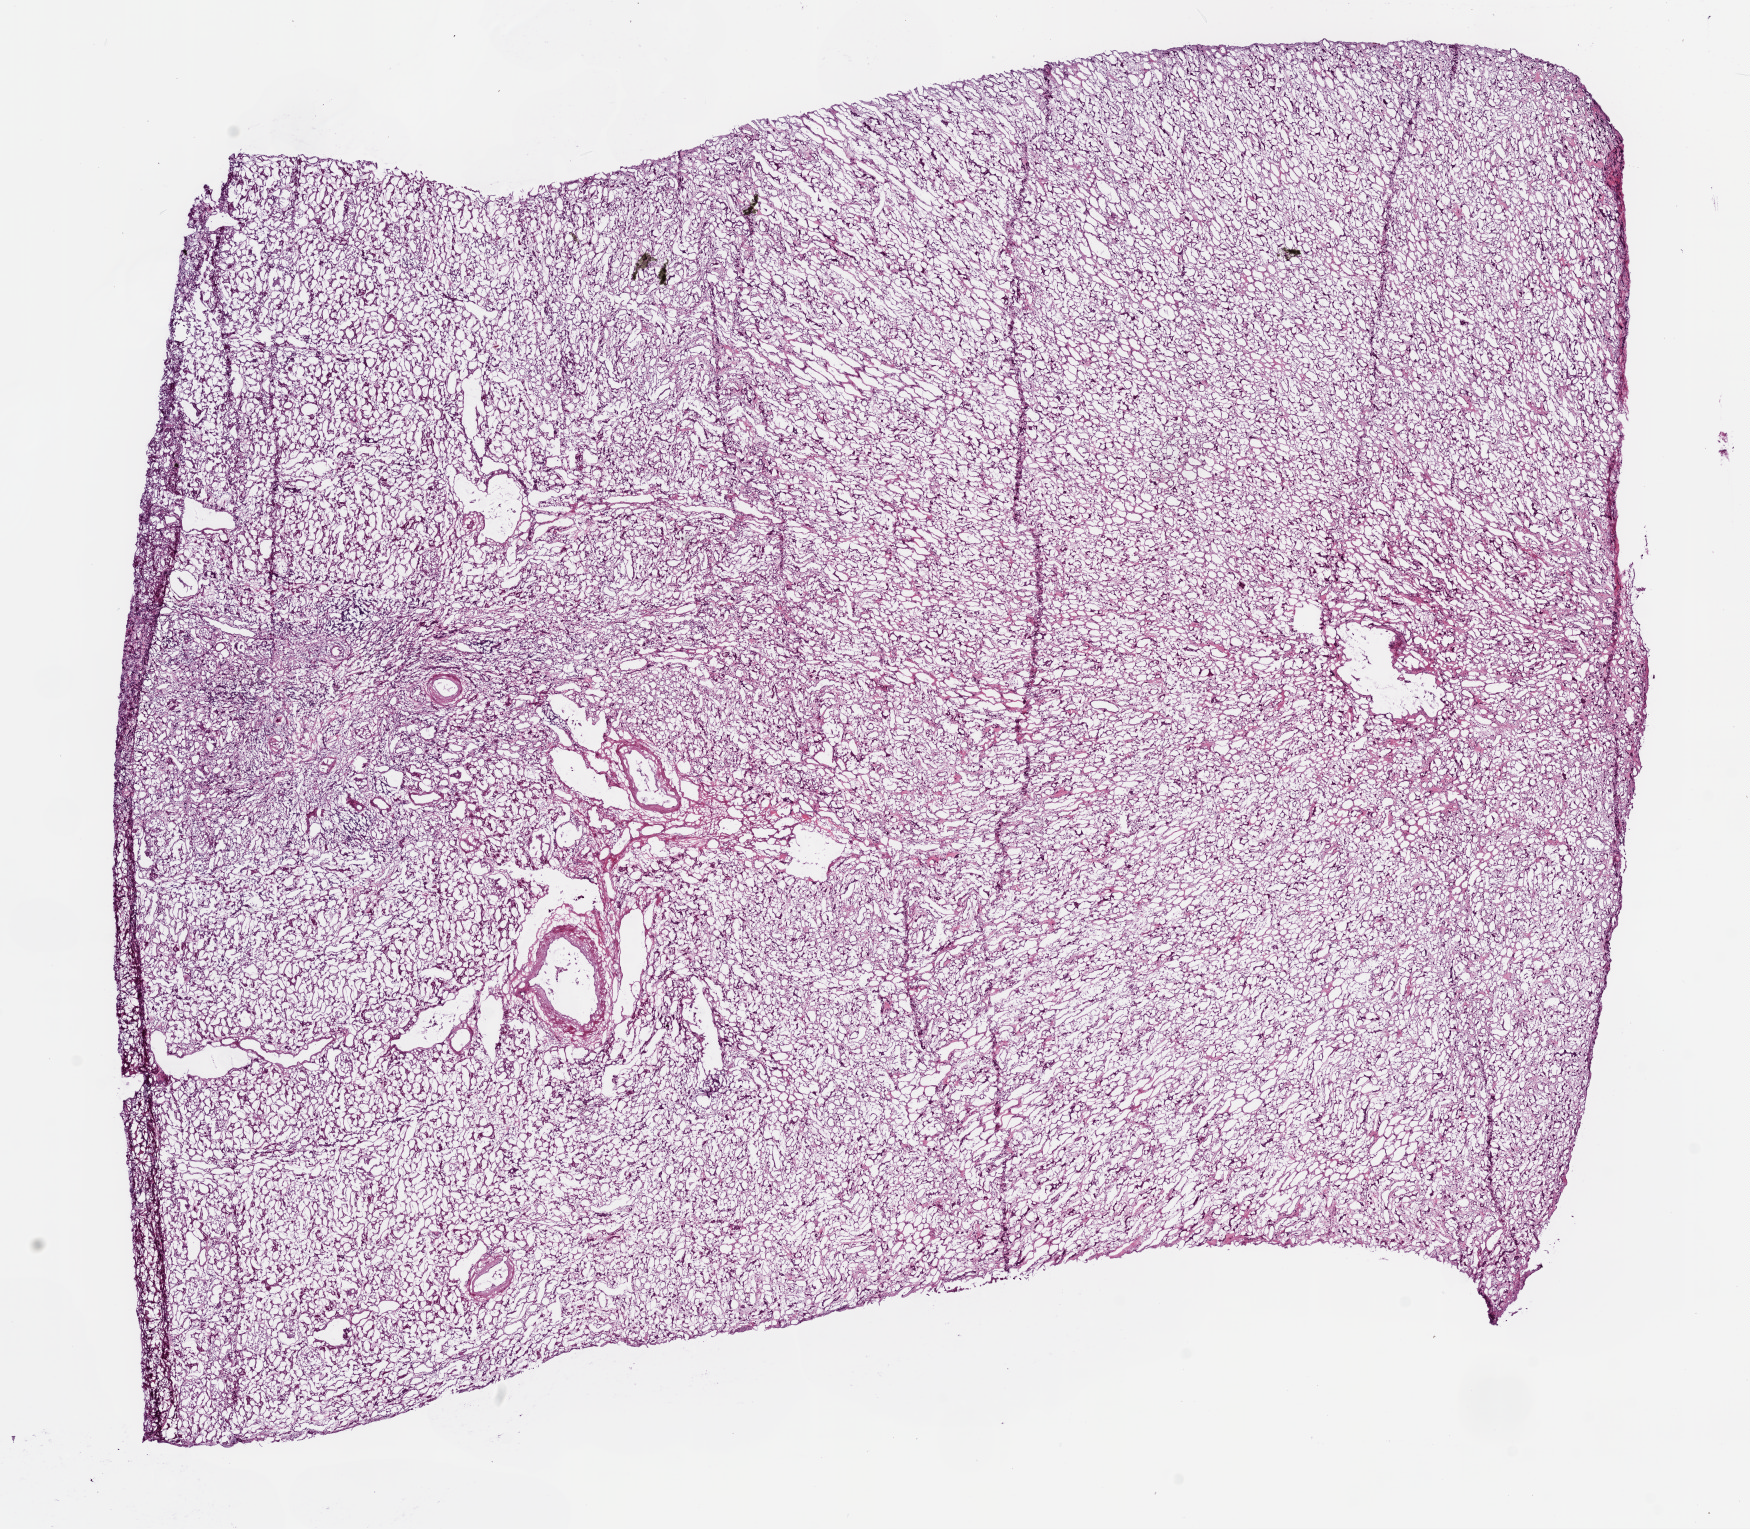
Whole-slide histology image, Hematoxylin and eosin (H&E) stained, low-resolution overview of the scanned area, about 14.0 x 12.3 mm (from a 20x scan); frozen section; kidney, solid tissue normal (non-tumour tissue) sample. Female, age 65 years at initial diagnosis.
This section: solid tissue normal sample (biorepository sample class). Patient diagnosis: Clear cell adenocarcinoma, NOS.